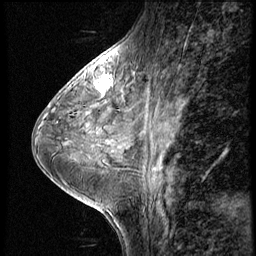
Breast MRI (dynamic contrast-enhanced), one sagittal slice. Slice 24 of 56 in the series (ordered by position). 4 images stored at this slice position (order not interpretable as contrast timing). 1.5 T. TE 4.2 ms, TR 8.9 ms. 2.5 mm slice thickness. 256 × 256 image matrix, field of view 200 × 200 mm. Patient: female, 38 years. From the clinical record (not read from this slice): setting: breast cancer imaged before/during neoadjuvant chemotherapy; receptor status: triple-negative.
Outlined on this slice (semi-automatic segmentation, software-assisted and operator-edited):
- analysis volume of interest (the breast-tissue region the enhancement analysis was run in; not a lesion): bounding box (x1, y1, x2, y2) in pixels: (88, 73, 115, 102)
- tumour enhancement mask (voxels above the 140 % enhancement threshold inside the analysis volume of interest): (94, 76, 110, 93)